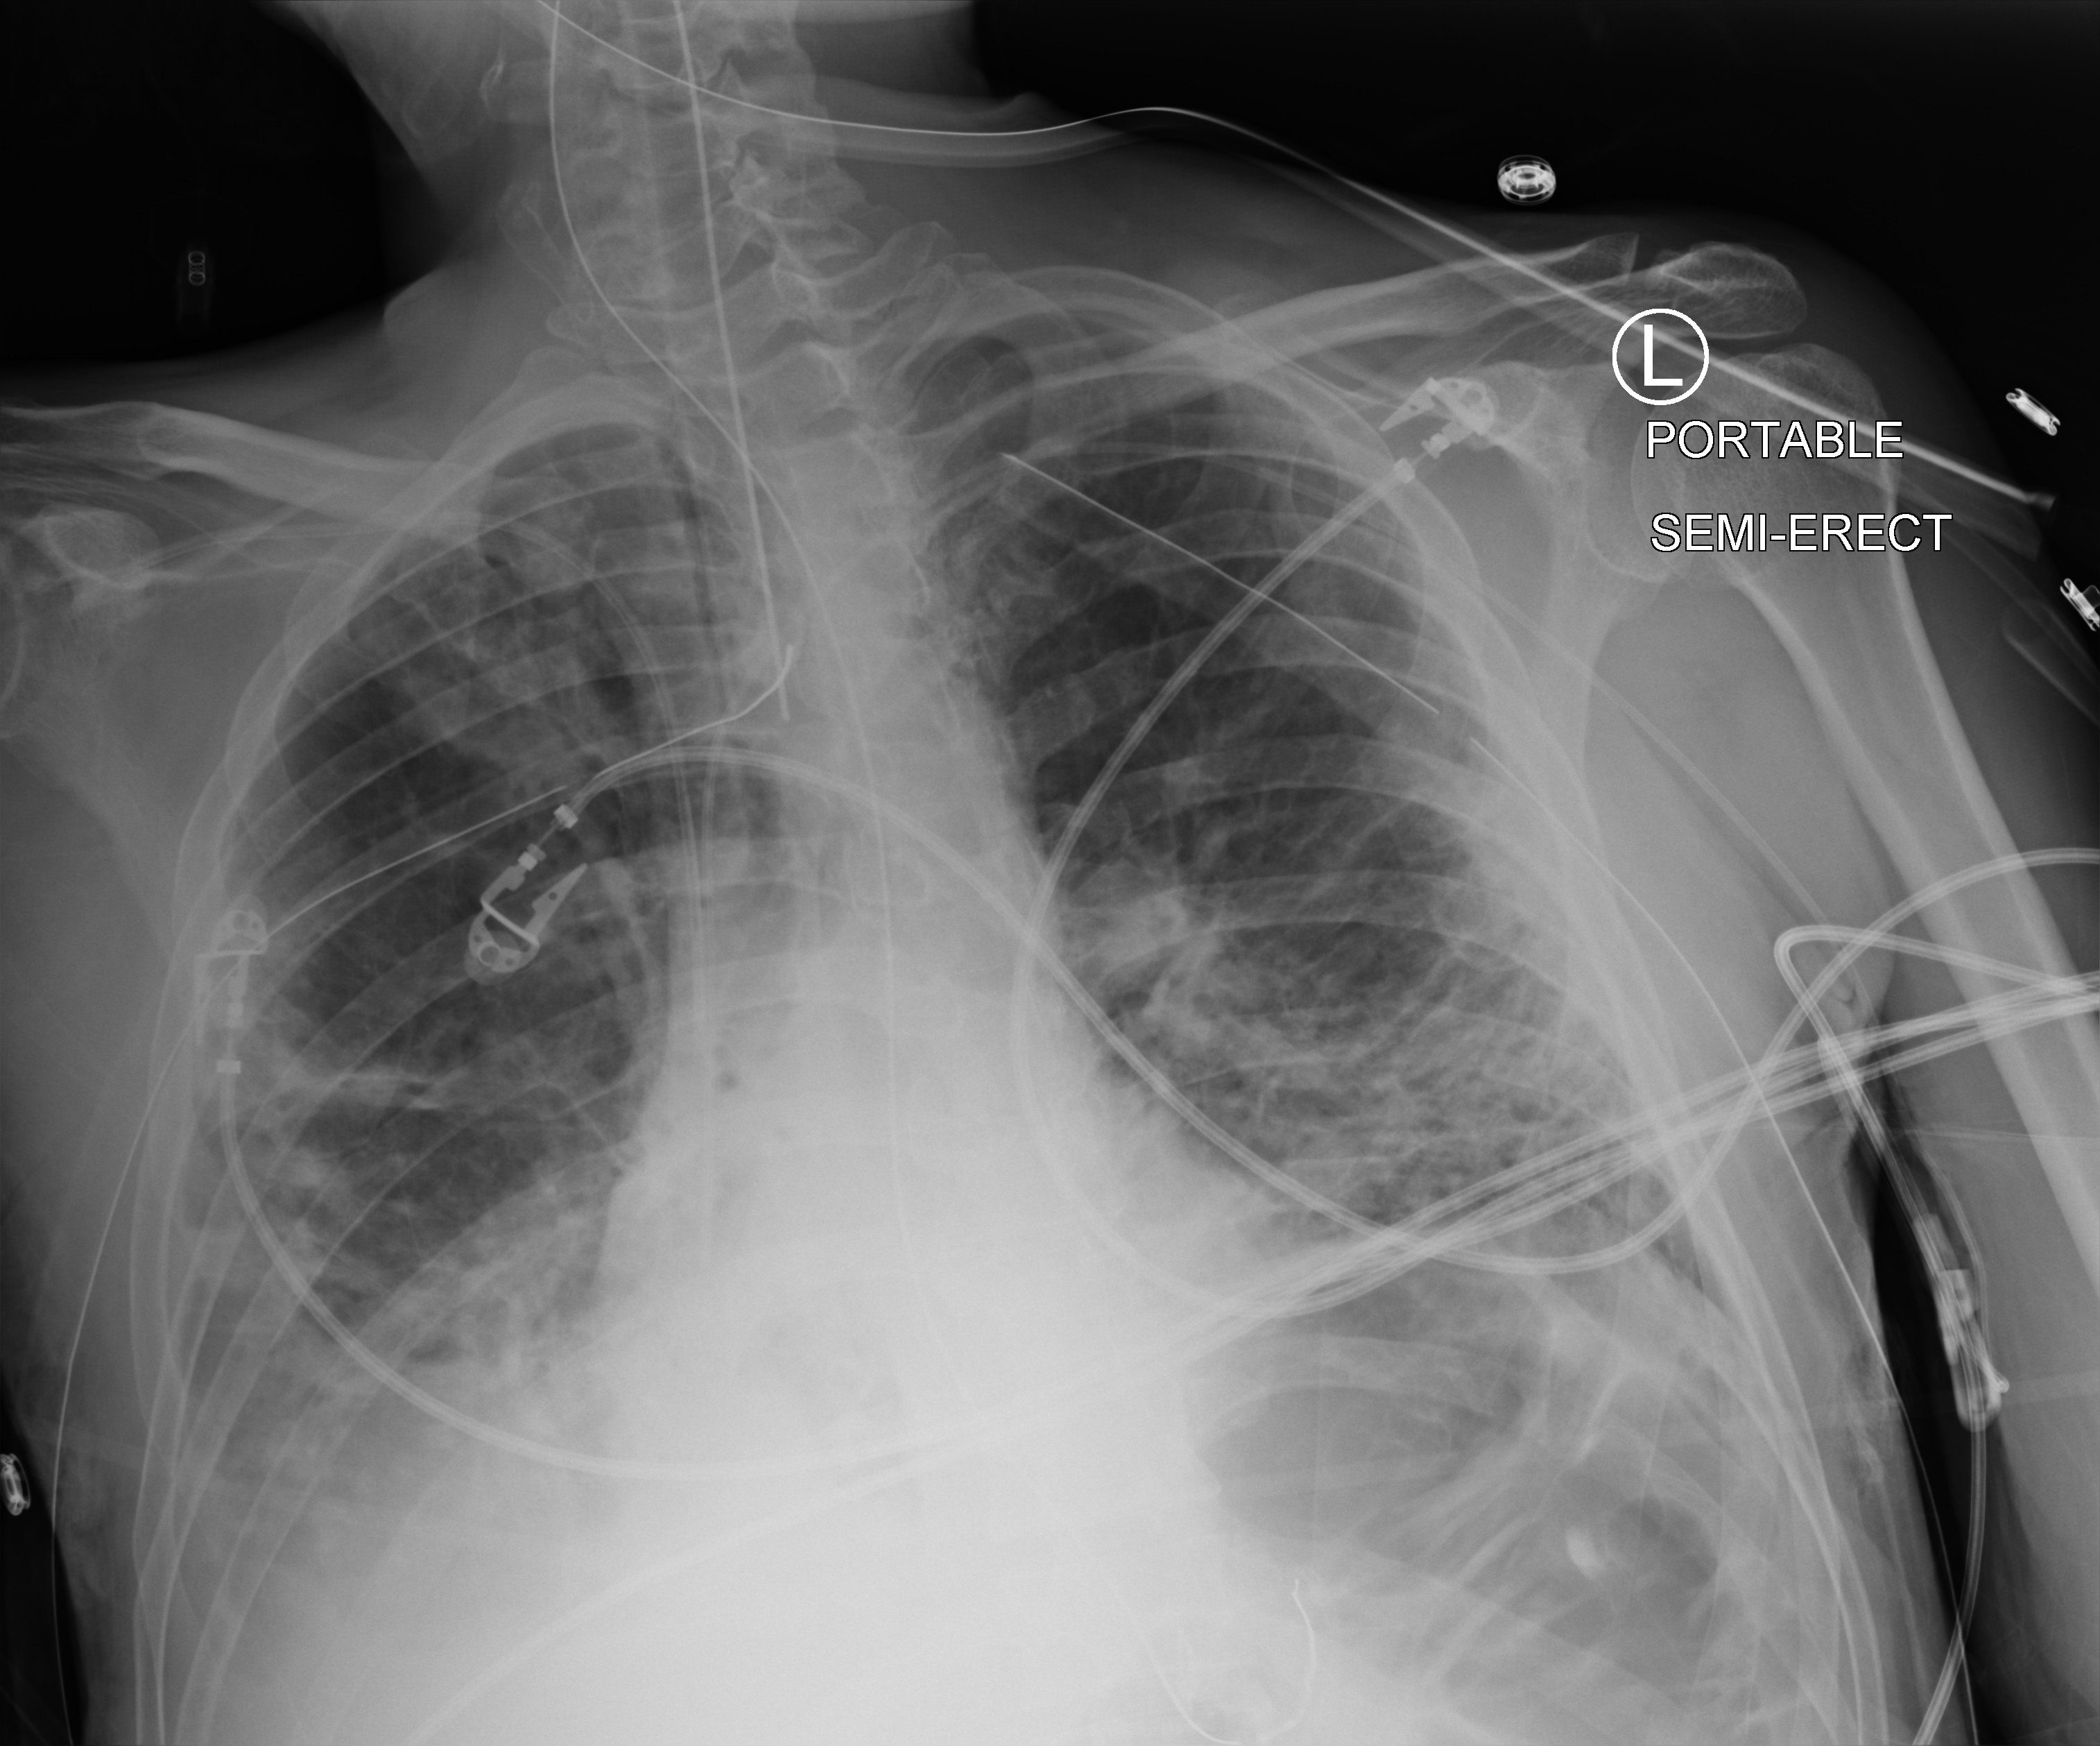
Bedside chest radiograph (computed radiography), anteroposterior (AP) projection. Patient hospitalised with COVID-19; male, aged 18–59 years.
Hospital-stay facts (about this admission, not read from this image; timing relative to this image not recorded): admitted to intensive care during this hospital stay: yes.